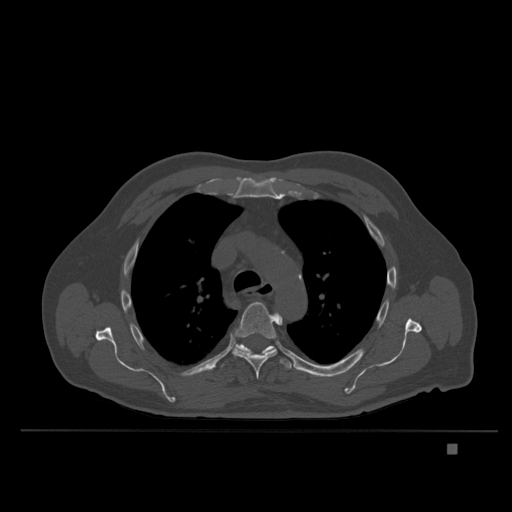
CT including the spine, one axial slice; slice 271 of 435 in the series (ordered by position); bone window (W 1800 / L 400 HU); 1.5 mm slice thickness; 512 × 512 image matrix. Patient: male, 73 years. From the clinical record (not read from this slice): primary cancer: skin.
Annotated regions visible in this slice (semi-automatic segmentation, software-assisted and operator-edited):
- T5 vertebra: bounding box (x1, y1, x2, y2) in pixels: (232, 302, 283, 379)
- T6 vertebra: (221, 345, 292, 369)